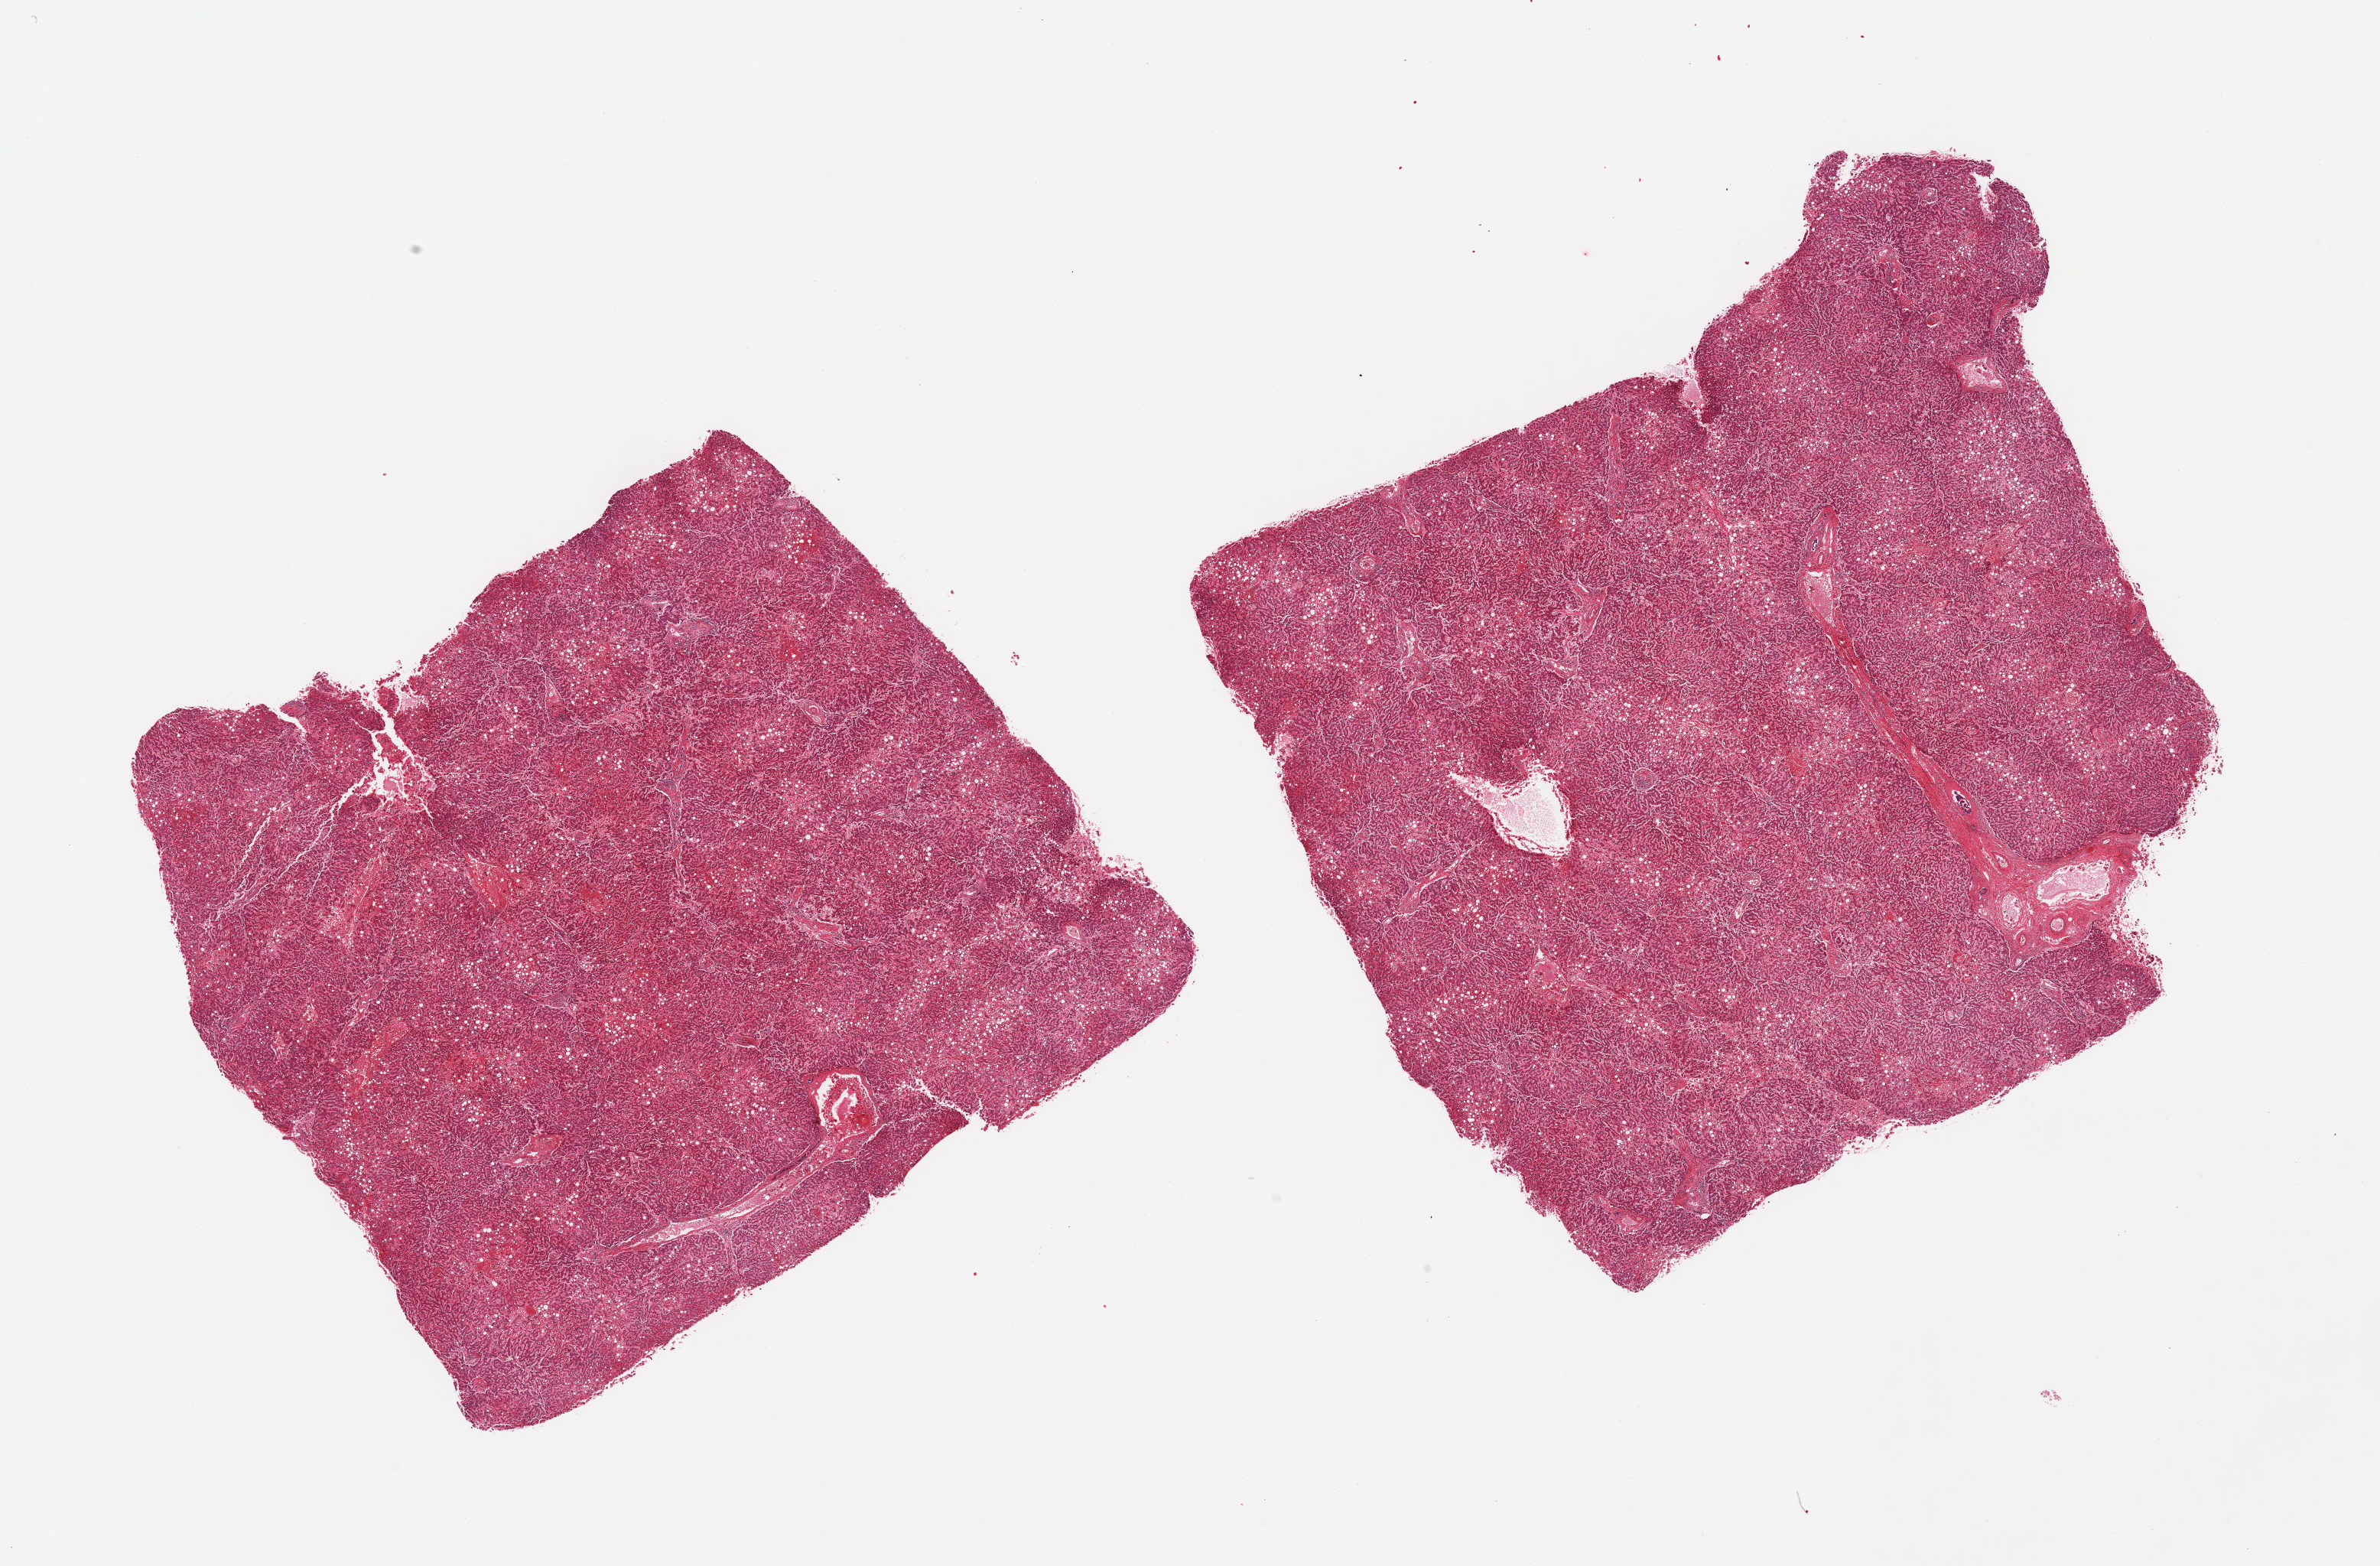
Hematoxylin and eosin (H&E) whole-slide image — a low-resolution overview of the entire scanned area, about 24.6 x 16.2 mm (from a 20x scan), PAXgene-fixed, paraffin-embedded tissue, sampled site (target tissue): liver, donor tissue sample. Female donor.
• review note (as recorded): 2 pieces; central congestion and moderate macrovesicular steatosis